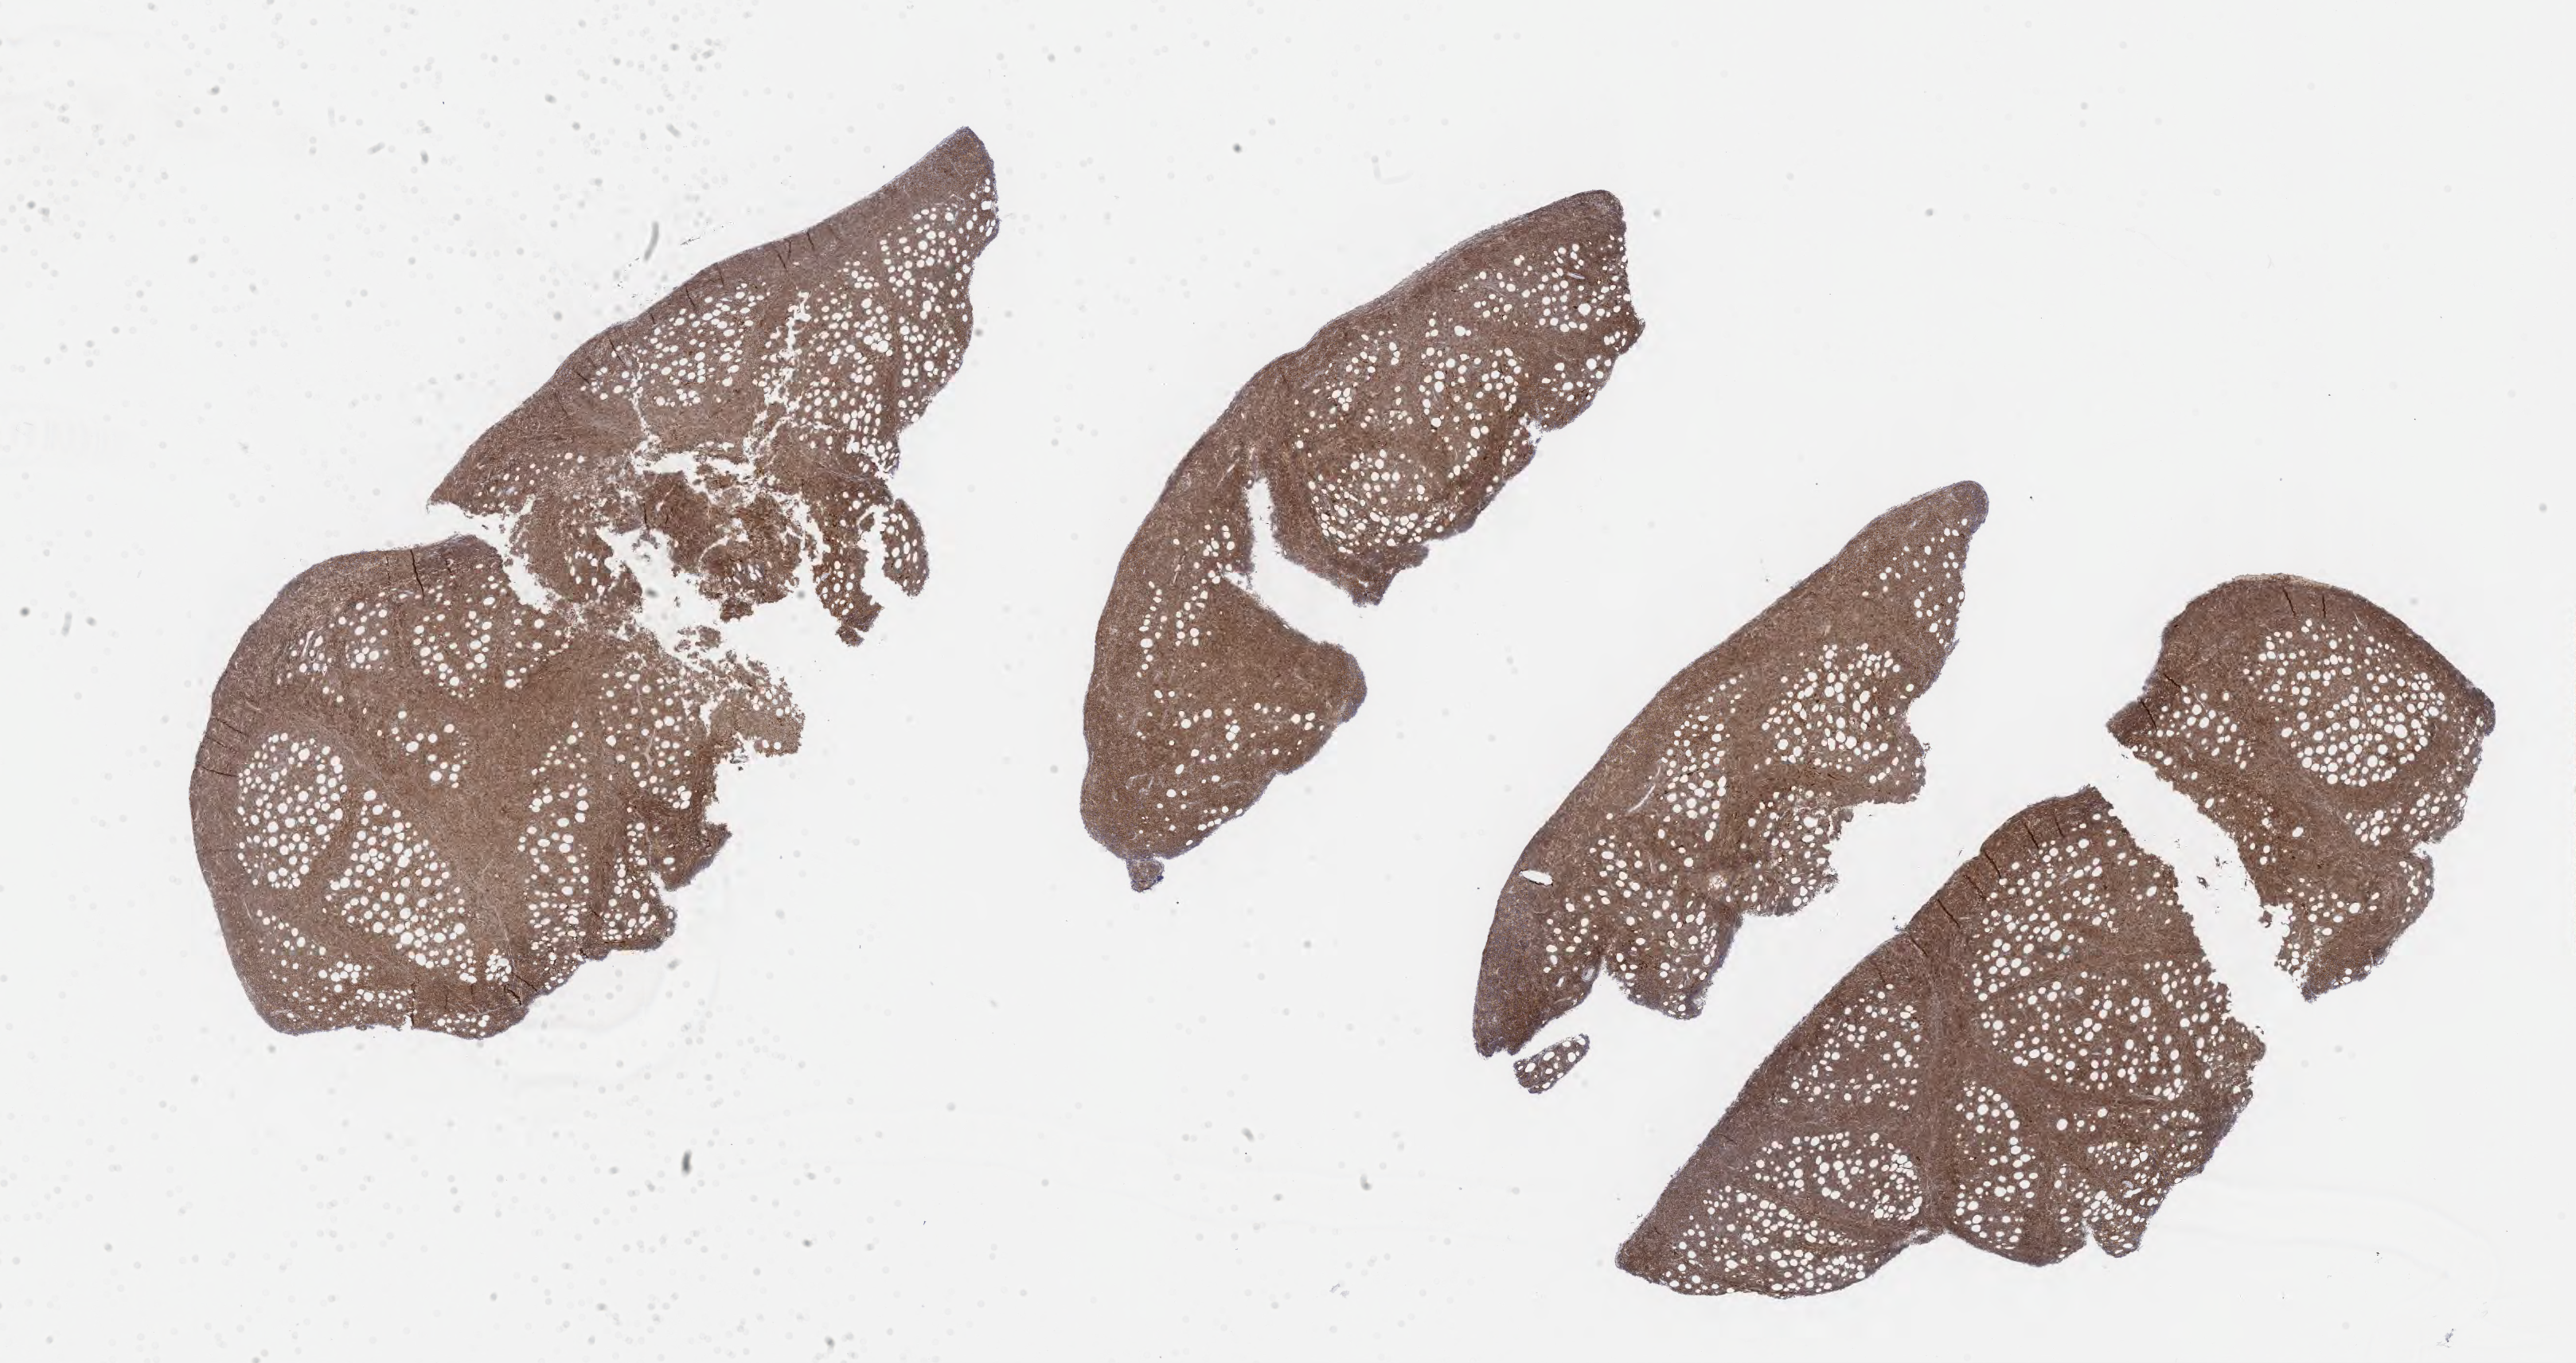
Immunohistochemistry (IHC) whole-slide image stained for CD10 — a low-resolution overview of the entire scanned area, about 26.2 x 13.8 mm, tumor tissue. Male patient, aged 52.
Diagnosis: Diffuse large B-cell lymphoma, NOS.